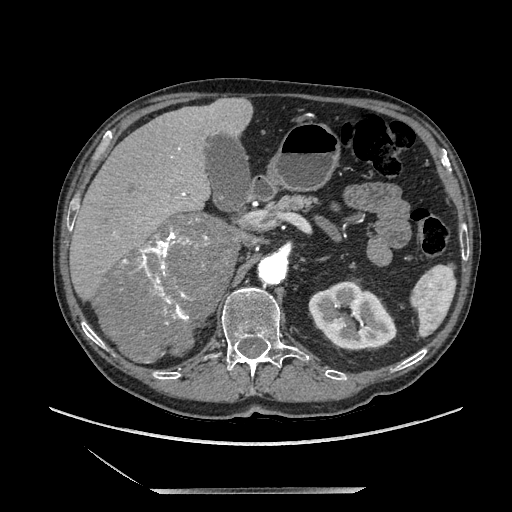
Contrast-enhanced abdominal CT, one axial slice. Position 124 of 243 along the scan axis. Soft-tissue window (W 400 / L 40 HU). 1.25 mm slice thickness. 512 × 512 image matrix. Male patient. Case-level facts recorded for this patient, not image findings: diagnosis: adrenocortical carcinoma; tumour side: right adrenal; tumour size at pathology: 16 cm; Ki-67 index: 17 %; stage (as recorded): 3.
Annotated regions visible in this slice (semi-automatic segmentation, software-assisted and operator-edited):
- mass: bounding box [x1, y1, x2, y2] px = [100, 214, 236, 361]